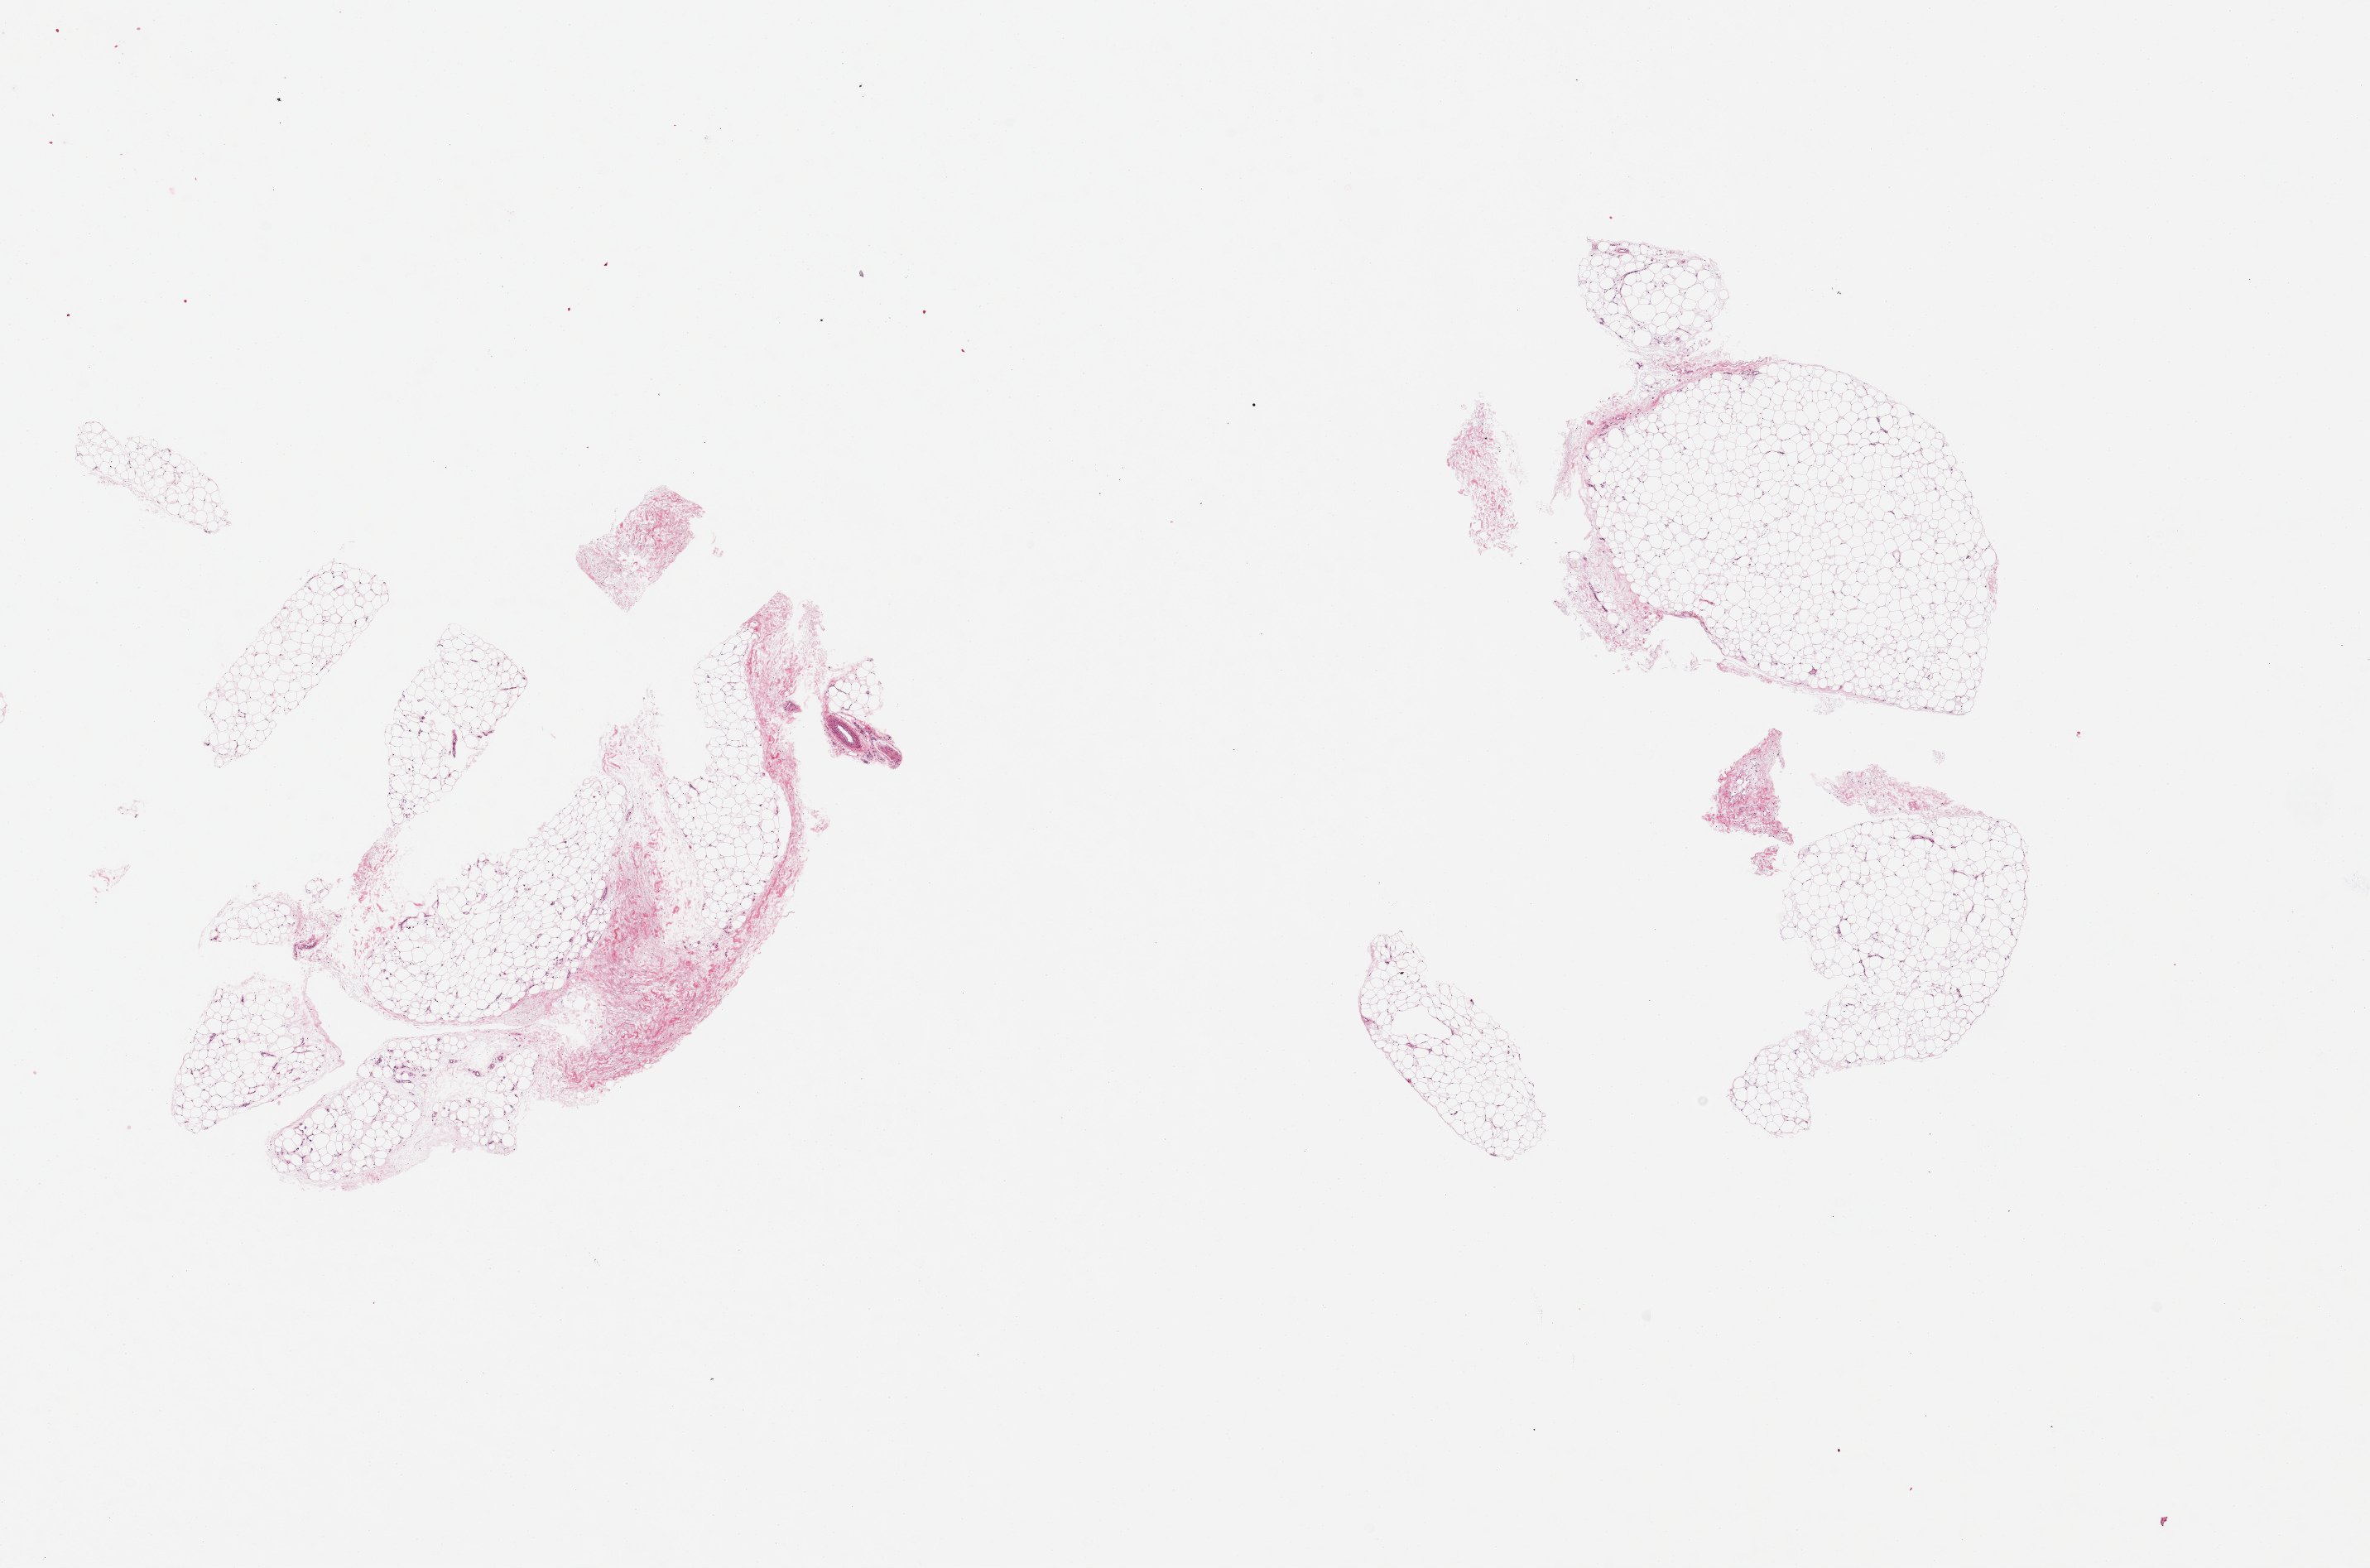
Whole-slide image, haematoxylin and eosin stain, brightfield — whole scanned area (about 22.6 x 15.0 mm) shown as a low-resolution overview. PAXgene-fixed paraffin-embedded (PFPE) section. Section of adipose tissue (target tissue). Tissue donor sample. Female donor.
Review note (as recorded): 3 pieces, up to 8x4mm.